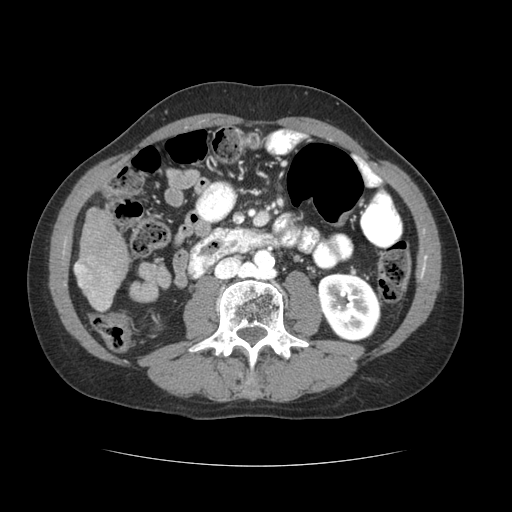
Contrast-enhanced abdominal CT (liver protocol), one axial slice; slice 11 of 69 in the series (ordered by position); 120 kVp; soft-tissue window (W 400 / L 40 HU); 2.5 mm slice thickness; 512 × 512 image matrix, field of view 360 × 360 mm. Case-level facts recorded for this patient, not image findings: diagnosis: hepatocellular carcinoma (patient treated with transarterial chemoembolisation; whether this scan precedes or follows treatment is not stated here); TNM stage (as recorded): Stage-II; Child-Pugh class: B; tumour differentiation: poorly differentiated; tumour nodularity: multinodular.
Annotated regions visible in this slice (semi-automatic segmentation, software-assisted and operator-edited):
- liver parenchyma outside the tumour (the mass and vessels are separate outlines, so this box may not span the whole liver): box from (x=74, y=208) to (x=128, y=310) px
- liver vessels: (x=75, y=263)–(x=111, y=310)